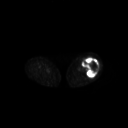
FDG PET of an extremity soft-tissue mass (from a PET/CT study), one axial slice; position 217 of 267 along the scan axis; 3.27 mm slice thickness; 128 × 128 image matrix, field of view 700 × 700 mm. Female patient, age 62 years. Case-level facts recorded for this patient, not image findings: histological type: undifferentiated – high grade; grade: high; site of the primary tumour: left thigh.
Annotated regions visible in this slice (expert contour drawn on MRI and transferred to this co-registered scan by the dataset authors):
- gross tumour volume including surrounding oedema: bounding box (x1, y1, x2, y2) in pixels: (82, 57, 99, 78)
- gross tumour volume (mass): (82, 57, 99, 78)